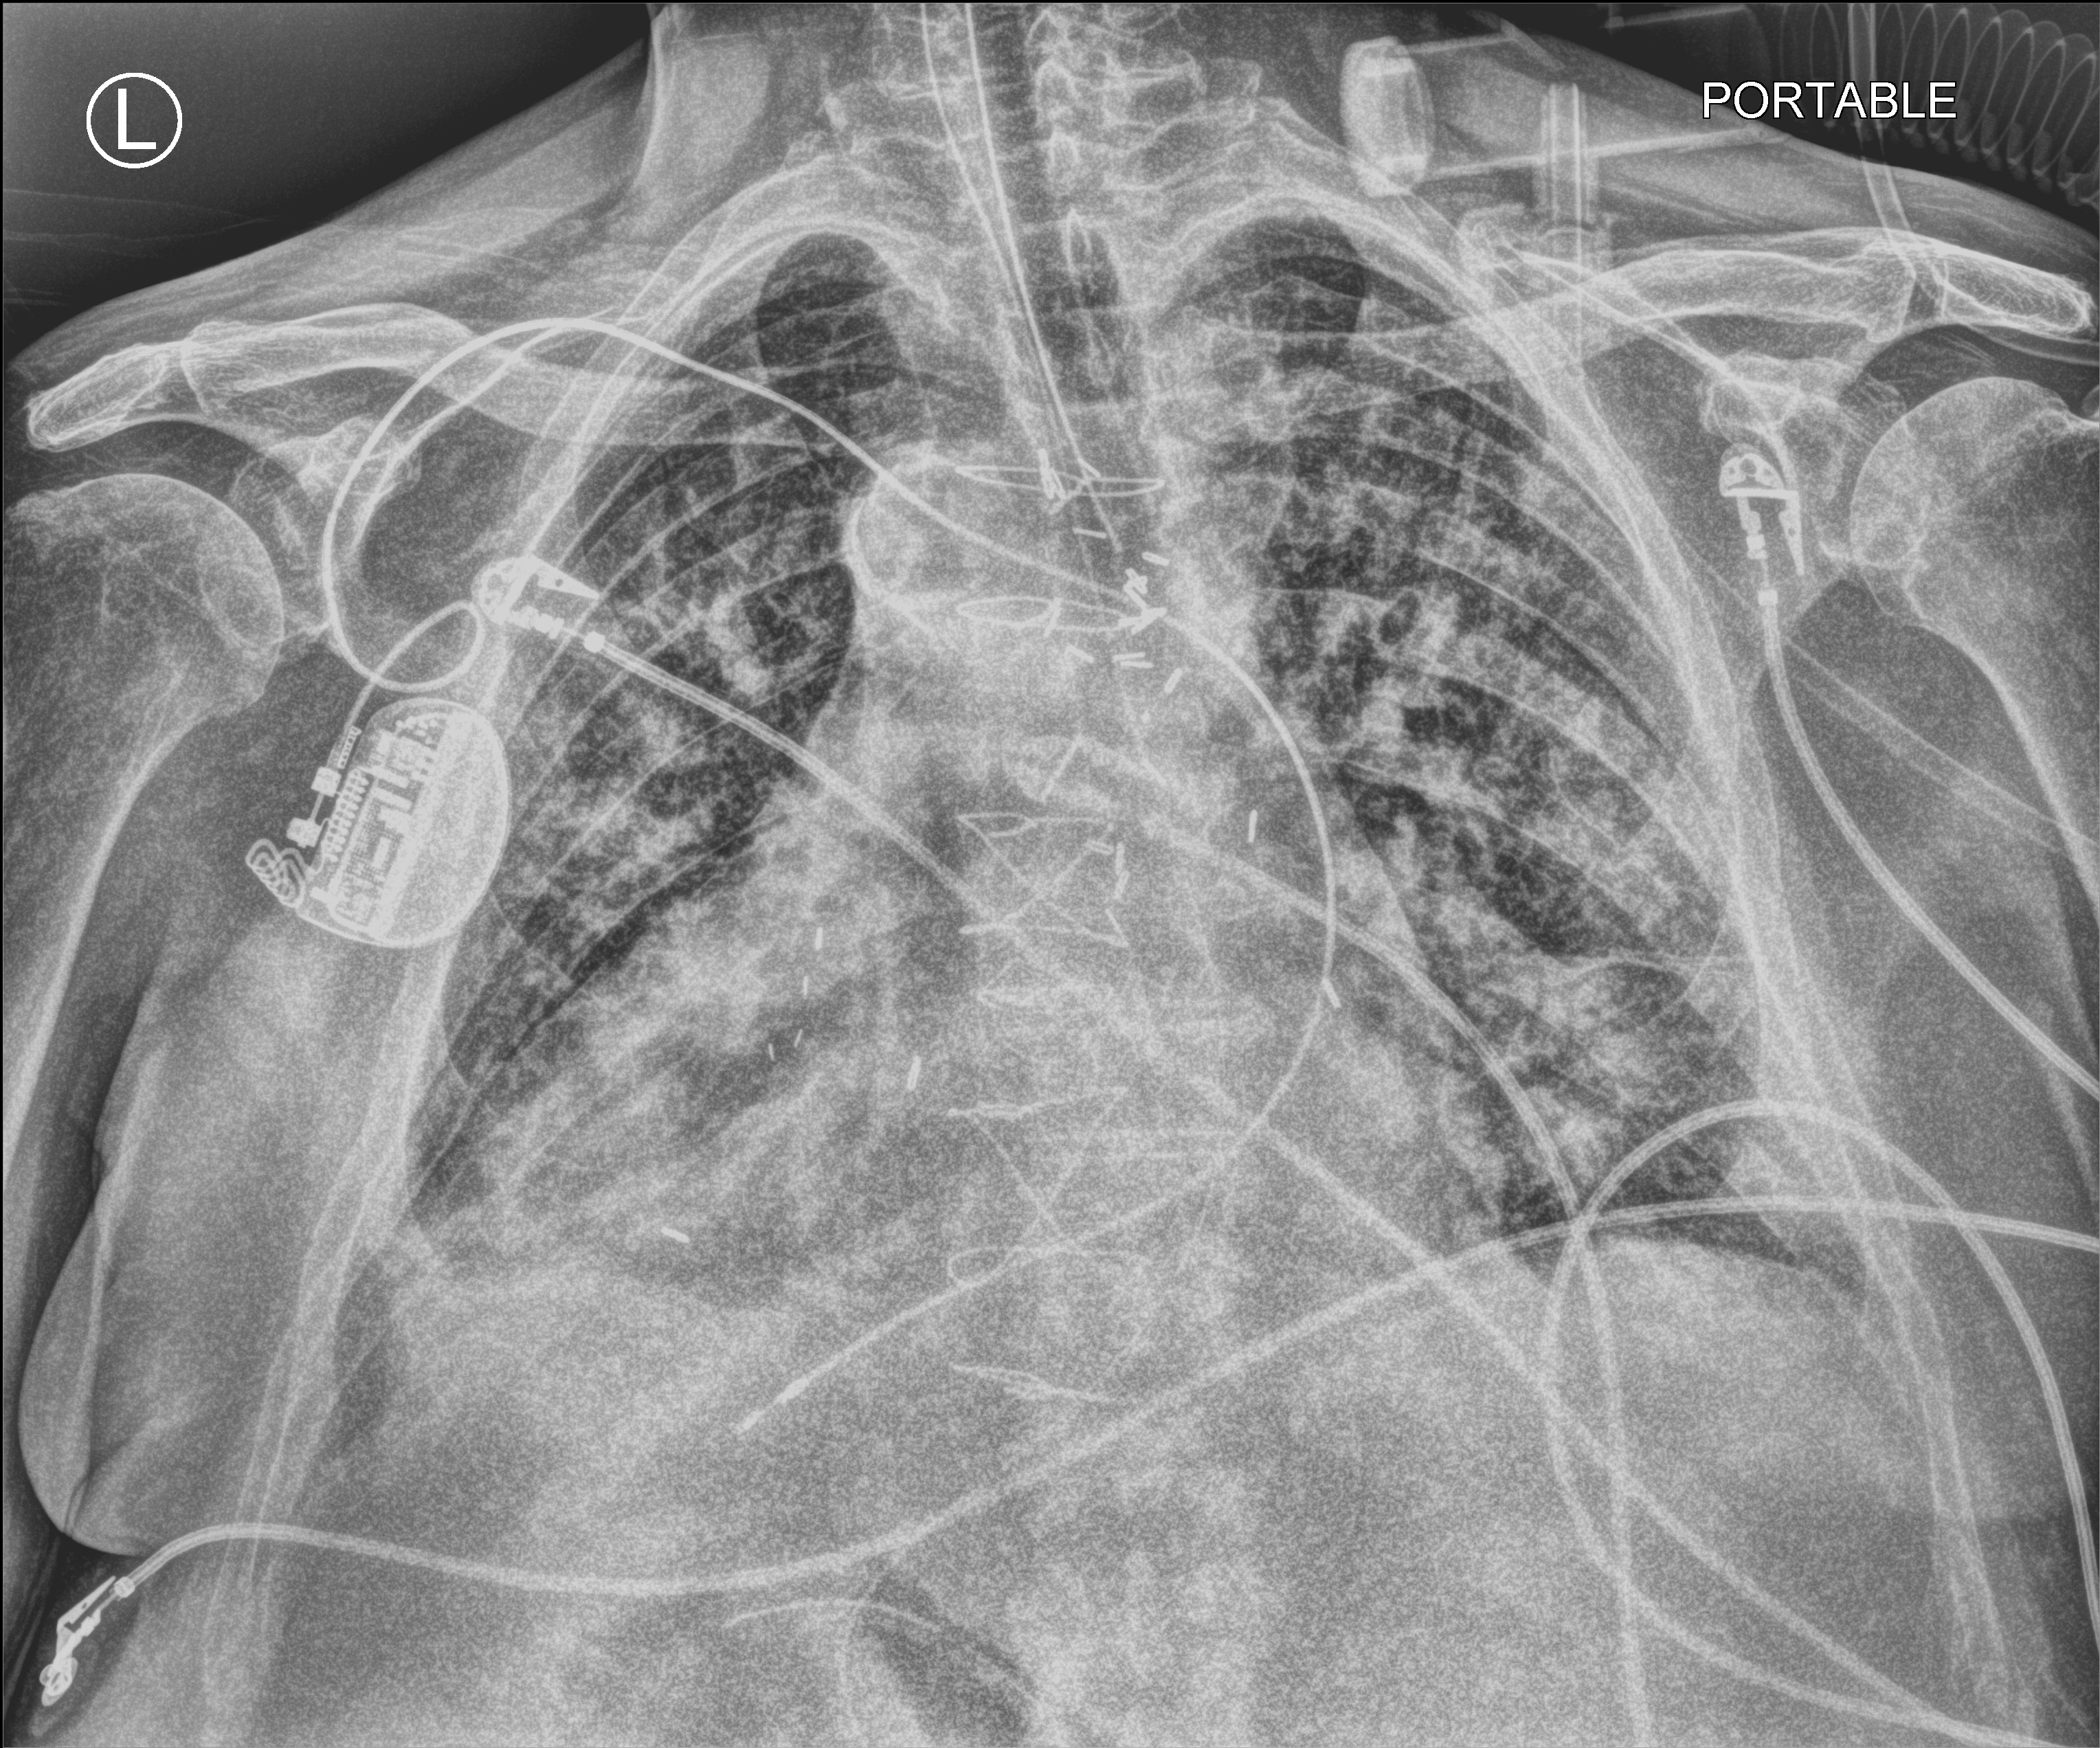
Bedside chest radiograph (computed radiography); anteroposterior (AP) projection. Patient hospitalised with COVID-19; male, aged 75–90 years.
From the hospital-stay record, not from the radiograph (when in the stay this image was taken is not recorded): length of hospital stay: 16 days.